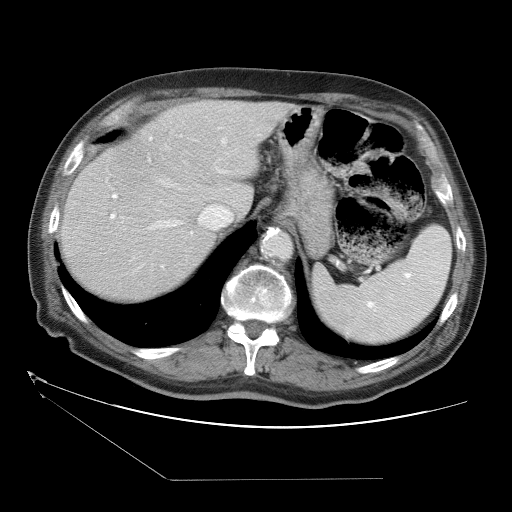
Contrast-enhanced abdominal CT (liver protocol), one axial slice. Slice 26 of 38 in the series (ordered by position). 120 kVp. One of 2 acquisitions stored at this slice position. Soft-tissue window (W 400 / L 40 HU). 512 × 512 image matrix. From the clinical record (not read from this slice): diagnosis: hepatocellular carcinoma (patient treated with transarterial chemoembolisation; whether this scan precedes or follows treatment is not stated here); TNM stage (as recorded): Stage-II; Child-Pugh class: A; tumour differentiation: moderately differentiated; tumour nodularity: multinodular.
Structures marked on this image (semi-automatically segmented with operator editing):
- abdominal aorta: bounding box (x1, y1, x2, y2) in pixels: (263, 234, 291, 261)
- liver parenchyma outside the tumour (the mass and vessels are separate outlines, so this box may not span the whole liver): (59, 100, 299, 298)
- liver vessels: (110, 137, 228, 268)